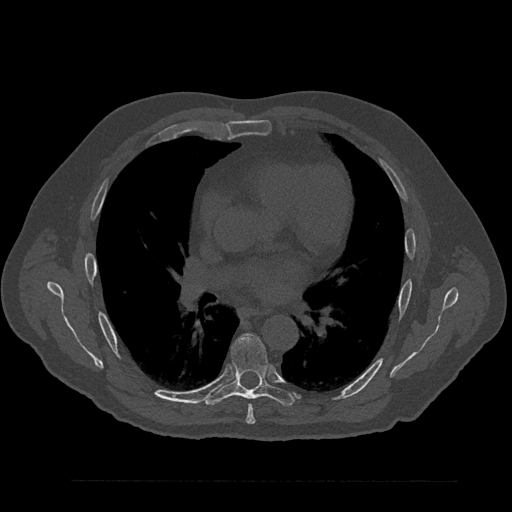
CT including the spine, one axial slice. Position 519 of 797 along the scan axis. Reconstruction kernel Br40s/3. 120 kVp. Bone window (W 1800 / L 400 HU). 0.5 mm slice thickness. 512 × 512 image matrix. Patient: male, 61 years. Case-level facts recorded for this patient, not image findings: primary cancer: prostate.
Outlined on this slice (semi-automatically segmented with operator editing):
- T6 vertebra: bounding box <246,405,256,424> (left, top, right, bottom; pixels)
- T7 vertebra: <204,334,295,406>